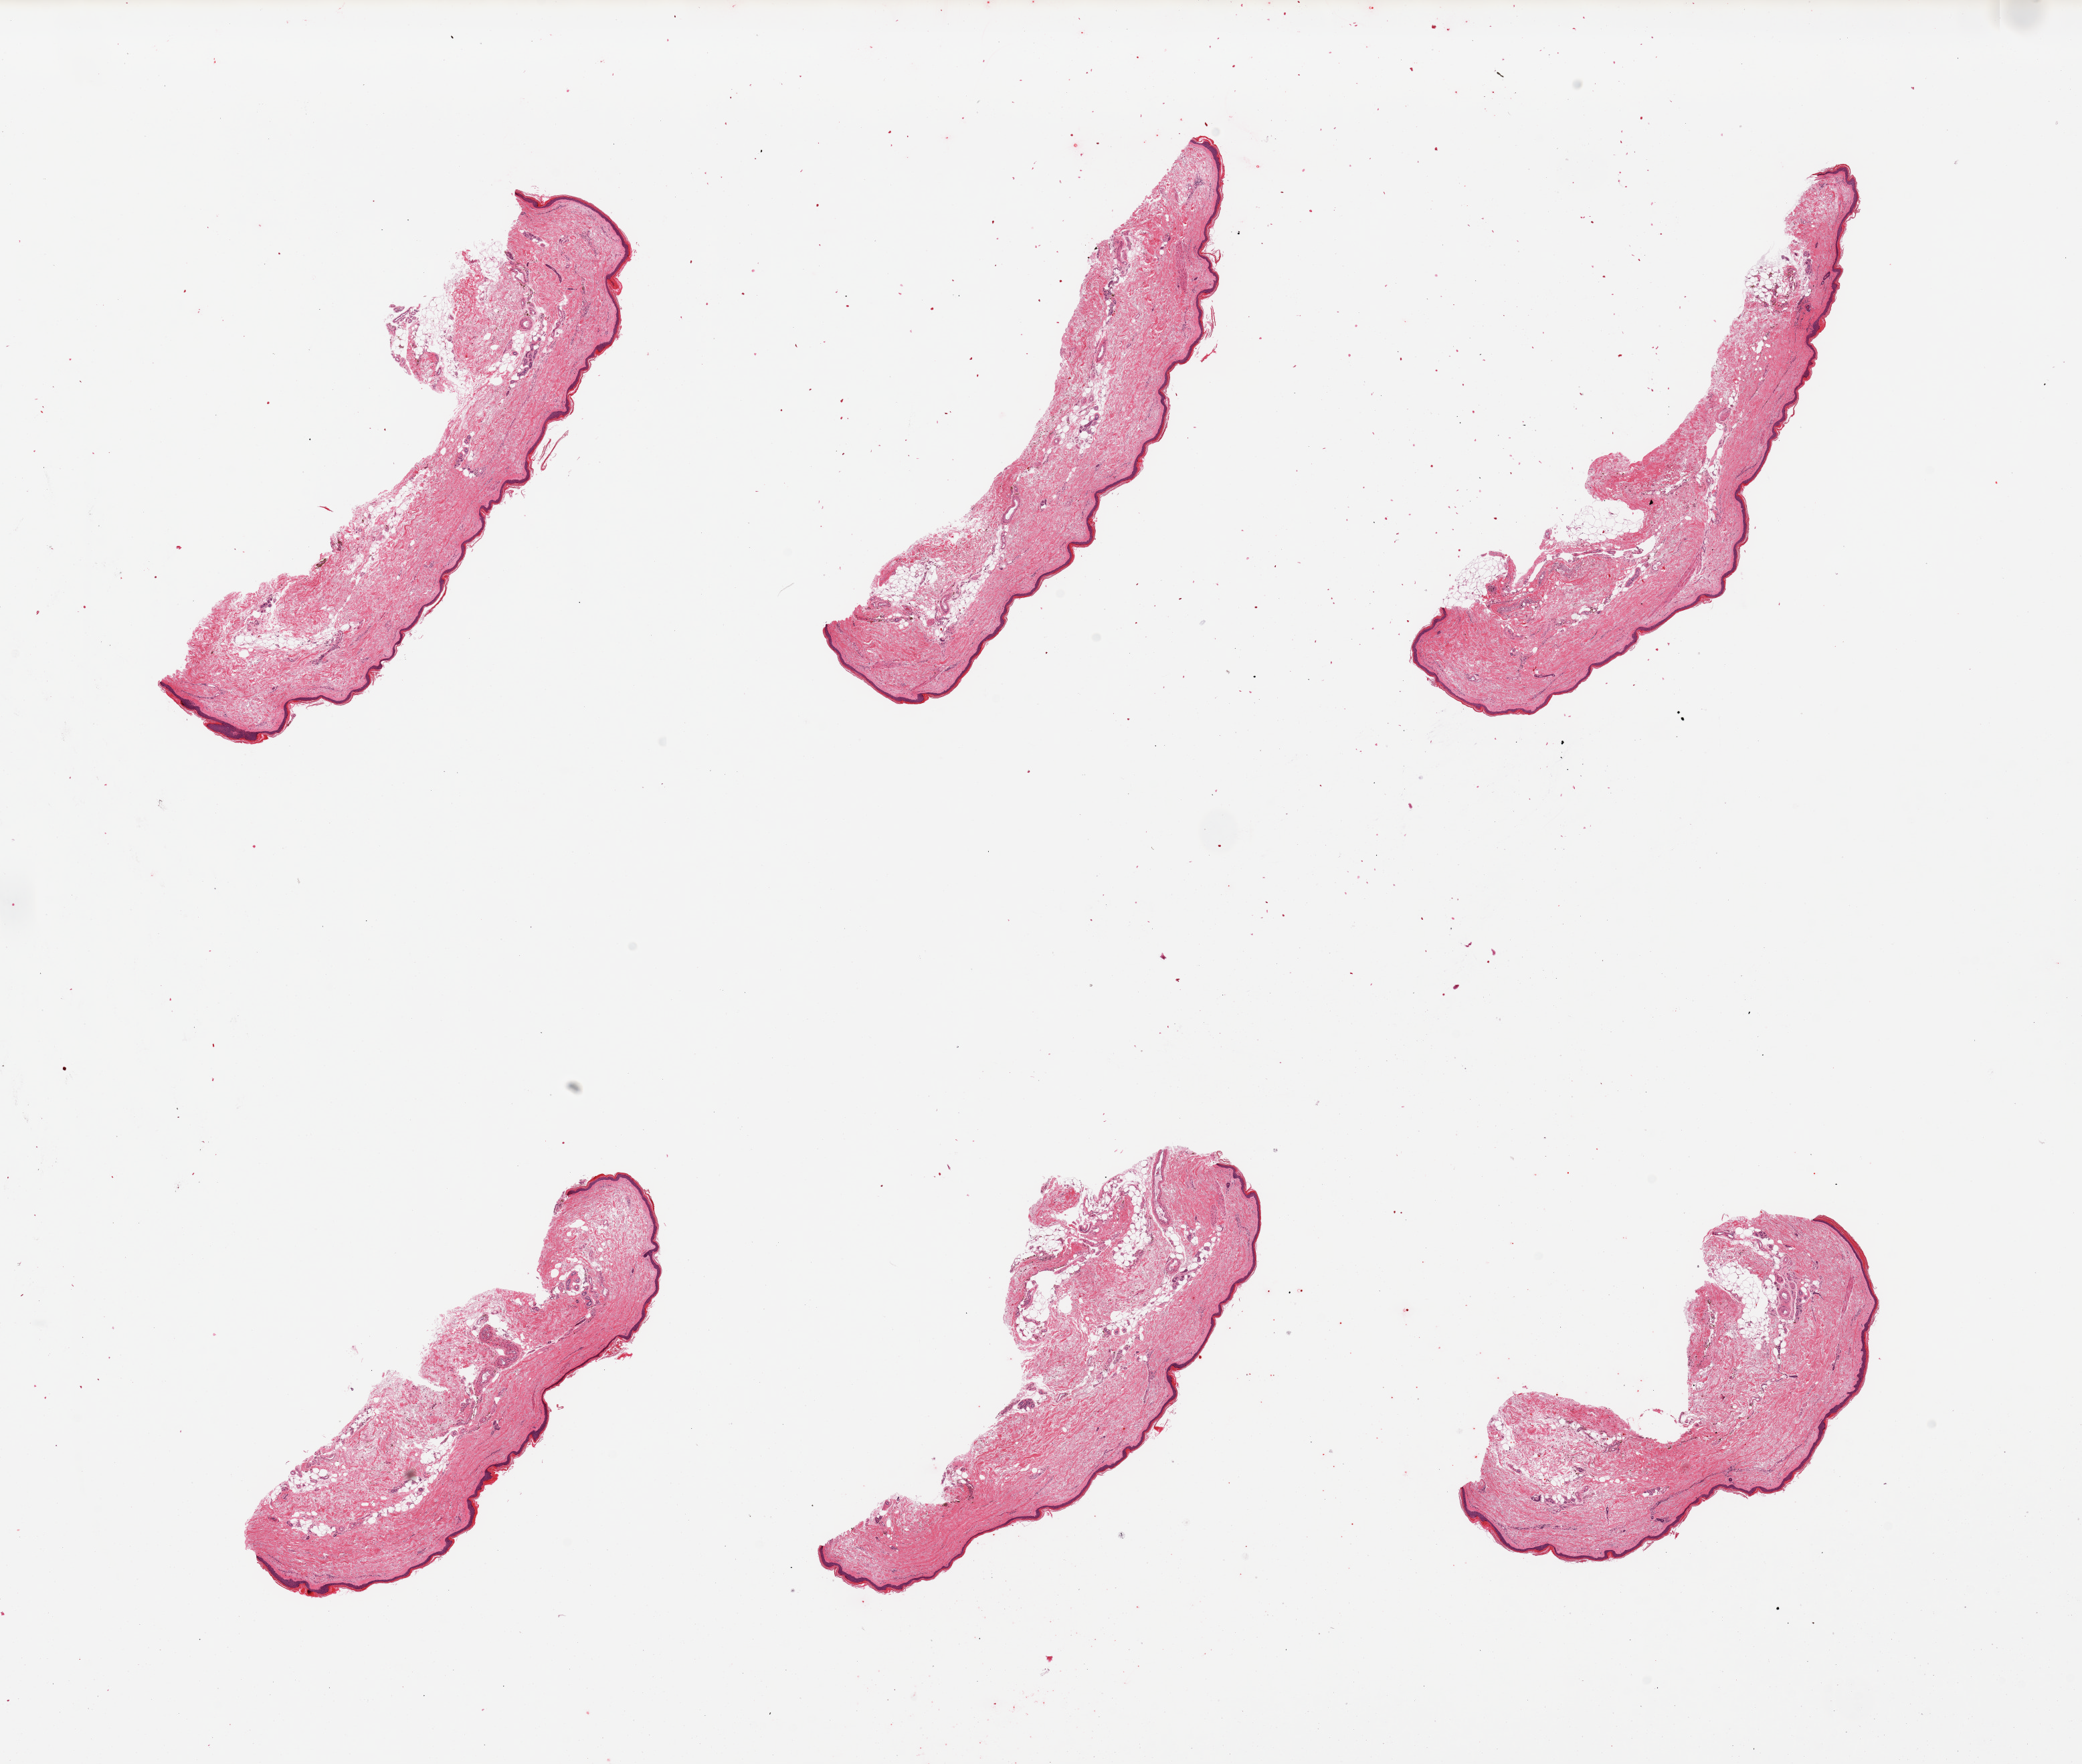
Digitized H&E-stained section, a low-resolution overview of the entire scanned area, about 24.6 x 20.9 mm, PAXgene-fixed paraffin-embedded (PFPE) section, section of skin of lower leg (target tissue), tissue donor sample. Donor sex: female.
Reviewer comment on this tissue sample: 6 pieces, well trimmed, squamous epithelium is 30-65 microns thick.